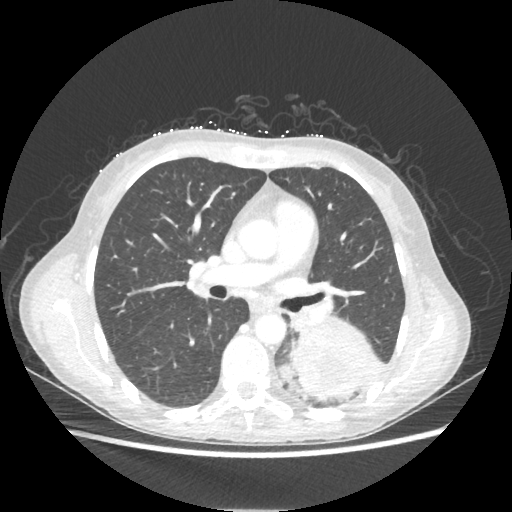
Chest CT, one axial slice; slice 121 of 221 in the series (ordered by position); 80 kVp; lung window (W 1500 / L -600 HU); 1.25 mm slice thickness; 512 × 512 image matrix. Female patient, age 53 years. From the clinical record (not read from this slice): clinical TNM (as recorded): T3 N0 M0.
Structures marked on this image (rectangle marked by the reading radiologist):
- lung tumour (recorded histology: adenocarcinoma): box from (x=290, y=317) to (x=378, y=402) px